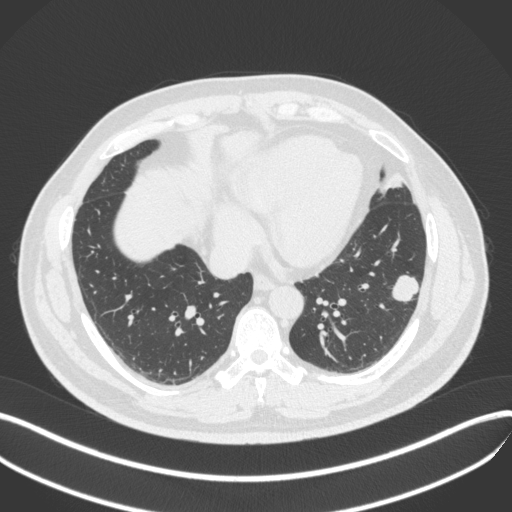
Chest CT, one axial slice; slice 146 of 420 in the series (ordered by position); reconstruction kernel B31f; lung window (W 1500 / L -600 HU); 512 × 512 image matrix, field of view 400 × 400 mm. Patient: male, 39 years. From the clinical record (not read from this slice): clinical TNM (as recorded): T2a N0 M0; histopathological grade: G2-3.
Annotated regions visible in this slice (bounding box drawn by a radiologist):
- lung tumour (recorded histology: adenocarcinoma): bounding box [x1, y1, x2, y2] px = [384, 268, 421, 305]